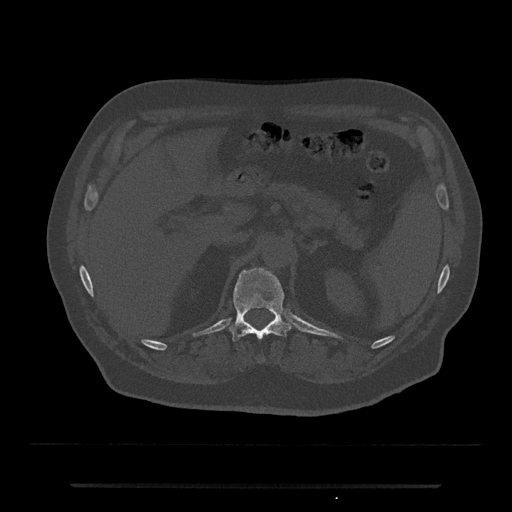
CT including the spine, one axial slice; position 595 of 797 along the scan axis; 120 kVp; bone window (W 1800 / L 400 HU); 512 × 512 image matrix, field of view 434 × 434 mm. Patient: male, 80 years. Case-level facts recorded for this patient, not image findings: primary cancer: prostate; vertebrae with lytic lesions (as recorded): L1, T11.
Annotated regions visible in this slice (semi-automatic segmentation, software-assisted and operator-edited):
- T12 vertebra: bounding box [x1, y1, x2, y2] px = [229, 267, 291, 342]